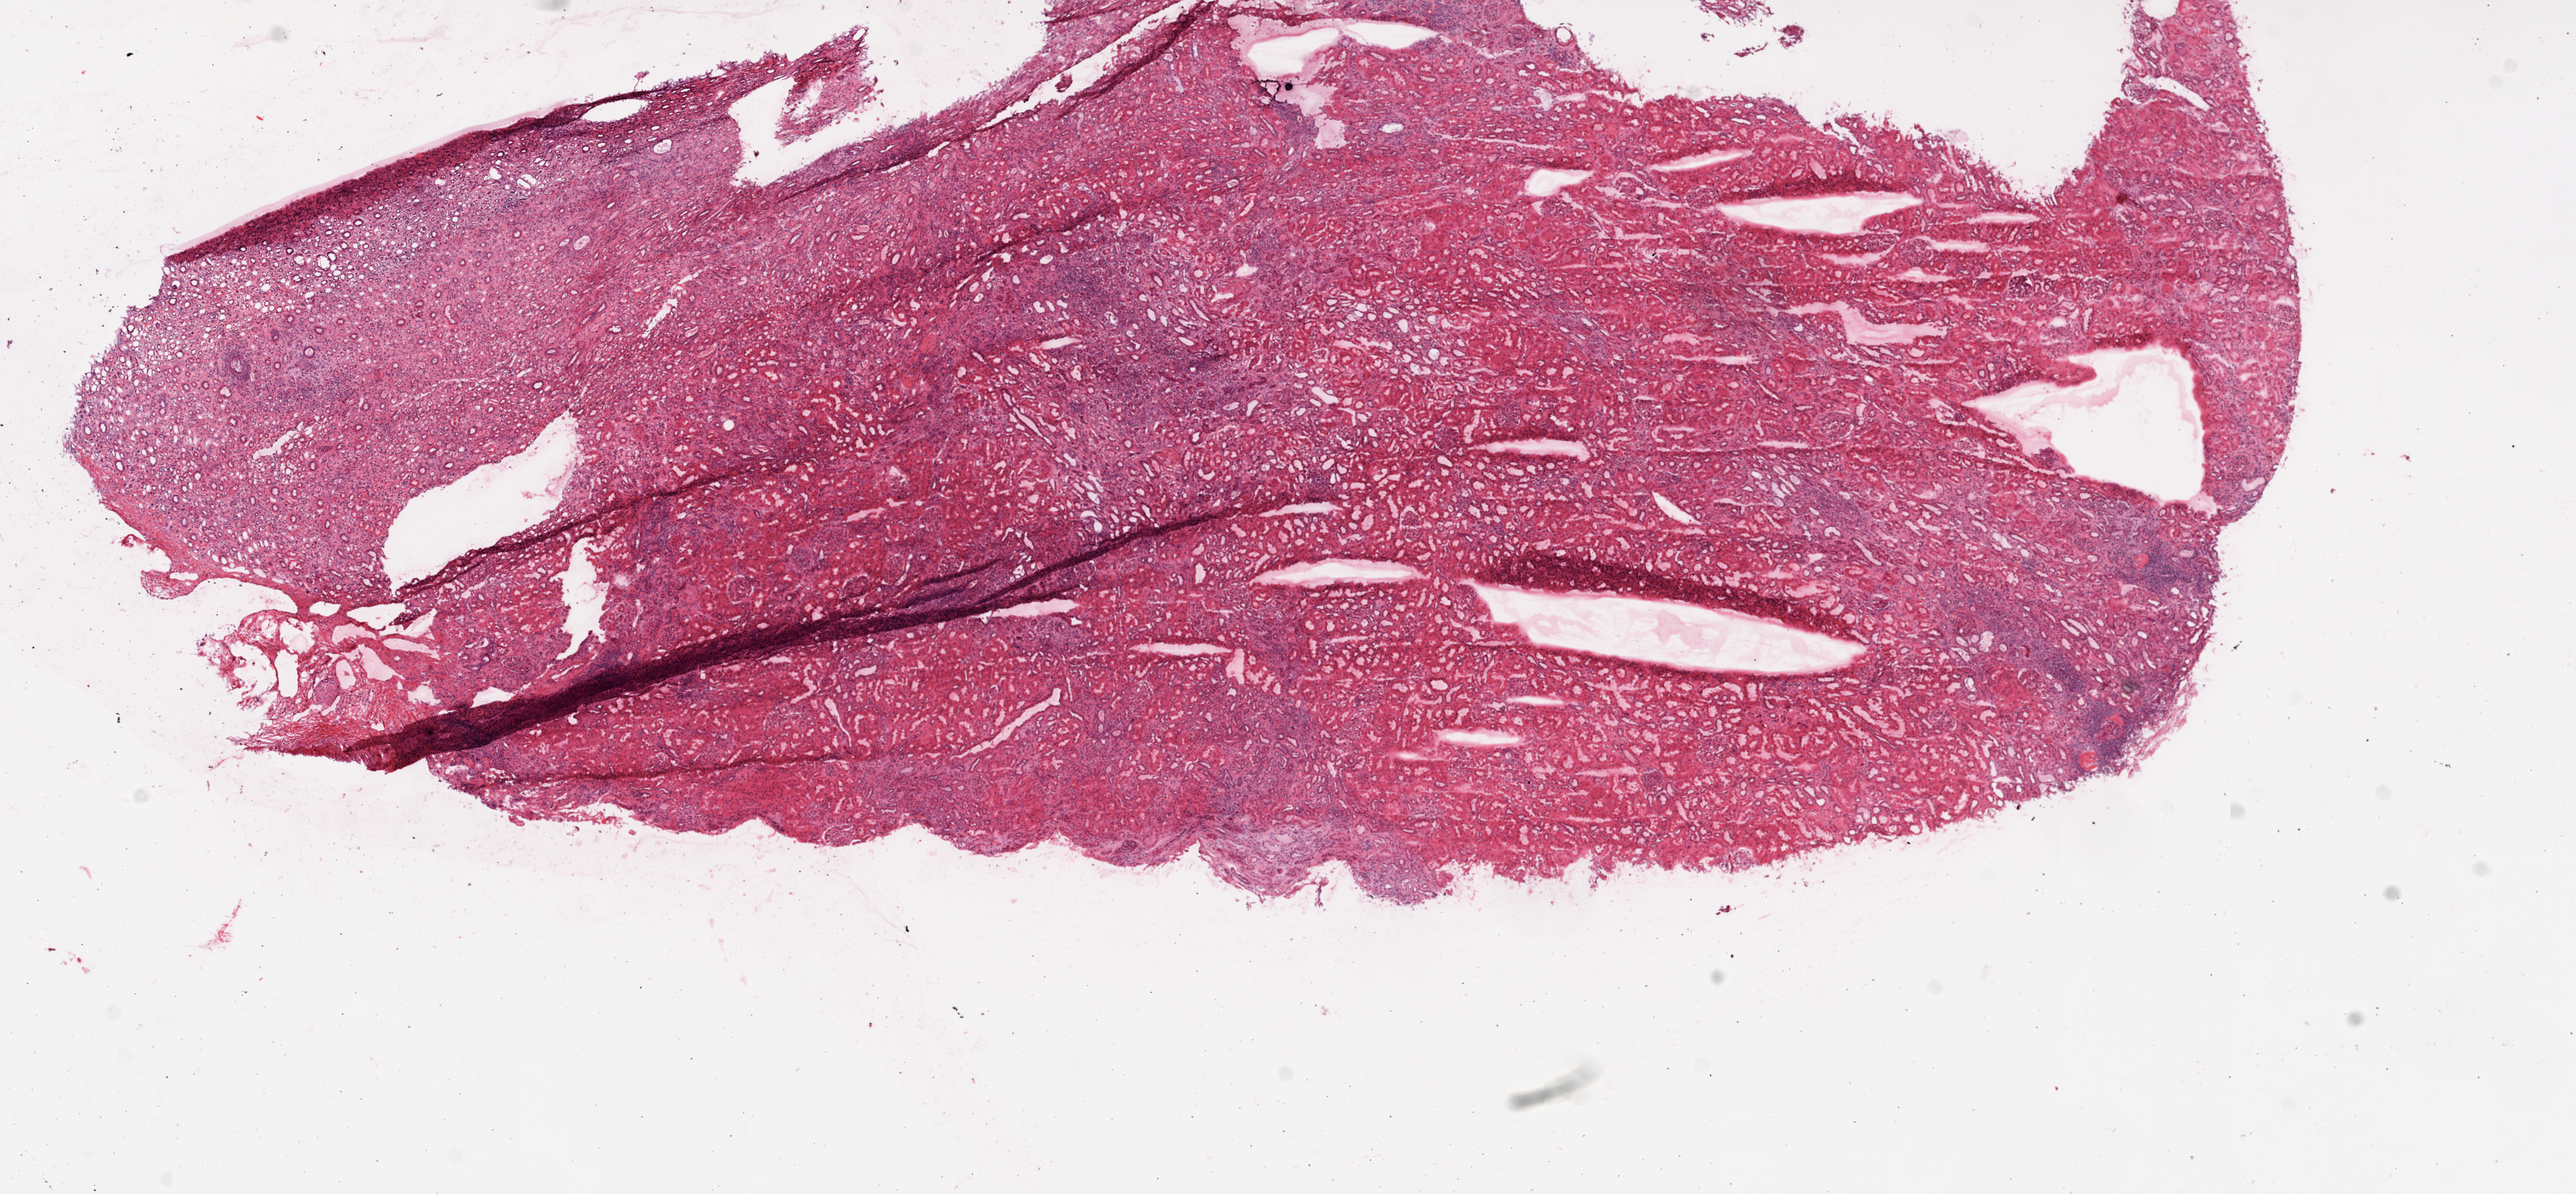
Whole-slide histology image, Hematoxylin and eosin (H&E) stained — low-resolution overview of the scanned area, about 15.0 x 7.0 mm (acquisition: 20x scan). Frozen section. Sample: solid tissue normal (non-tumour tissue), kidney. Patient: male, age at initial diagnosis 52 years.
This section: solid tissue normal sample (biorepository sample class). Patient diagnosis: Clear cell adenocarcinoma, NOS.